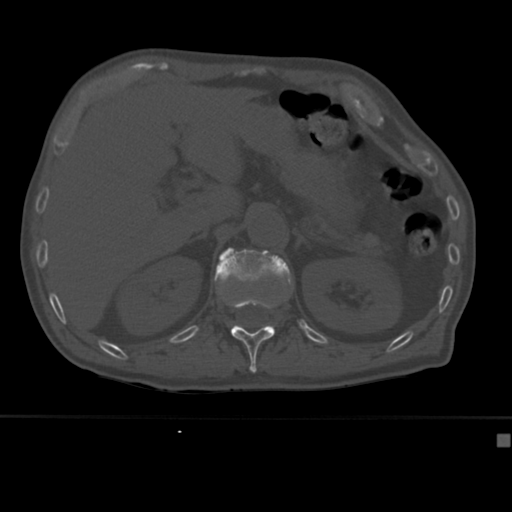
CT including the spine, one axial slice; slice 184 of 430 in the series (ordered by position); 120 kVp; bone window (W 1800 / L 400 HU); 512 × 512 image matrix, field of view 337 × 337 mm. Male patient, age 64 years. From the clinical record (not read from this slice): primary cancer: uterus.
Structures marked on this image (semi-automatically segmented with operator editing):
- L1 vertebra: bounding box <214,247,293,301> (left, top, right, bottom; pixels)
- T12 vertebra: <228,300,286,373>